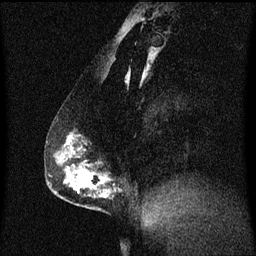
Breast MRI (dynamic contrast-enhanced), one sagittal slice. Position 29 of 60 along the scan axis. Dynamic contrast-enhanced series, image 2 of 3 at this slice position (ordered by acquisition). 1.5 T. TE 4.2 ms, TR 8.4 ms. 256 × 256 image matrix, field of view 200 × 200 mm. Patient: female, 40 years. Case-level facts recorded for this patient, not image findings: setting: breast cancer imaged before/during neoadjuvant chemotherapy; receptor status: triple-negative.
Outlined on this slice (semi-automatically segmented with operator editing):
- analysis volume of interest (the breast-tissue region the enhancement analysis was run in; not a lesion): box from (x=58, y=132) to (x=113, y=211) px
- tumour enhancement mask (voxels above the 70 % enhancement threshold inside the analysis volume of interest): (x=68, y=136)–(x=109, y=197)